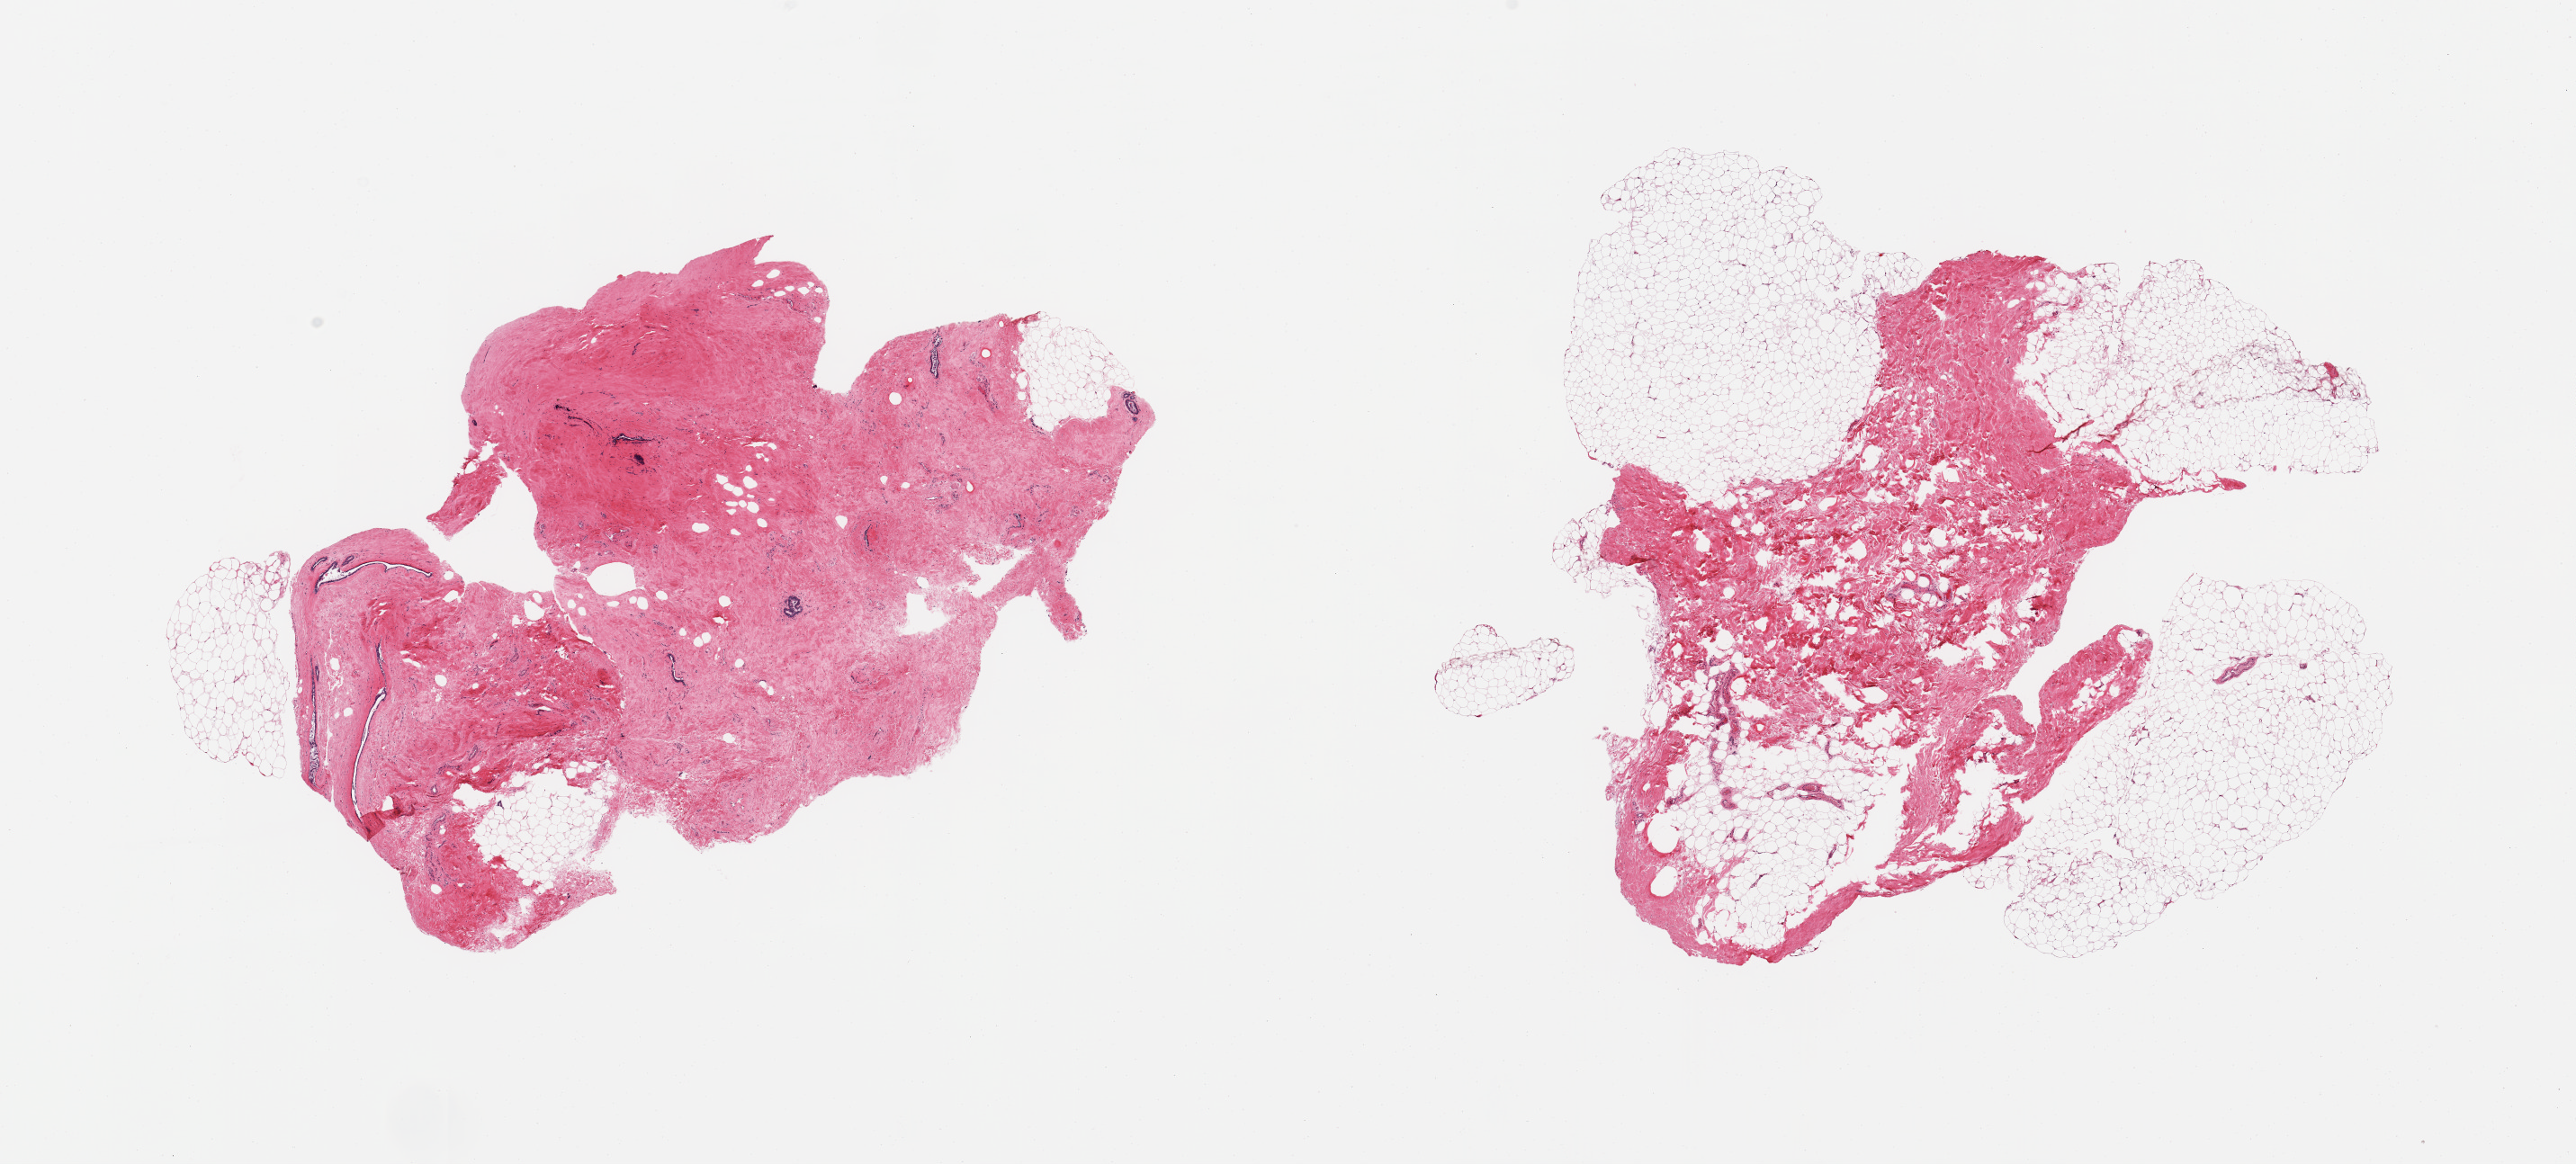
Whole-slide image, hematoxylin and eosin (H&E) stain, low-resolution overview of the scanned area, about 22.6 x 10.2 mm; PAXgene-fixed, paraffin-embedded tissue; sampled site (target tissue): breast; donor tissue sample. Male donor.
Review note (as recorded): 2 pieces; 1 piece shows dense fibrous stroma and scattered ductal structures, 2nd is composed of 50% fat and 50% fibrous tissue.